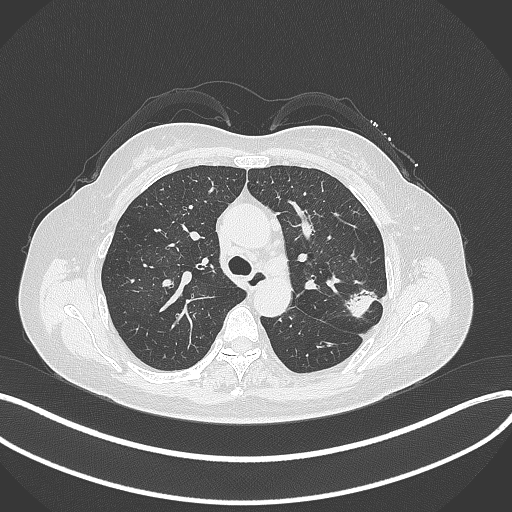
Chest CT, one axial slice; slice 222 of 319 in the series (ordered by position); reconstruction kernel B70f; lung window (W 1500 / L -600 HU); 1 mm slice thickness; 512 × 512 image matrix, field of view 400 × 400 mm. Patient: female, 60 years. From the clinical record (not read from this slice): clinical TNM (as recorded): T1c N0 M0.
Outlined on this slice (bounding box drawn by a radiologist):
- lung tumour (recorded histology: adenocarcinoma): bounding box <342,284,376,318> (left, top, right, bottom; pixels)